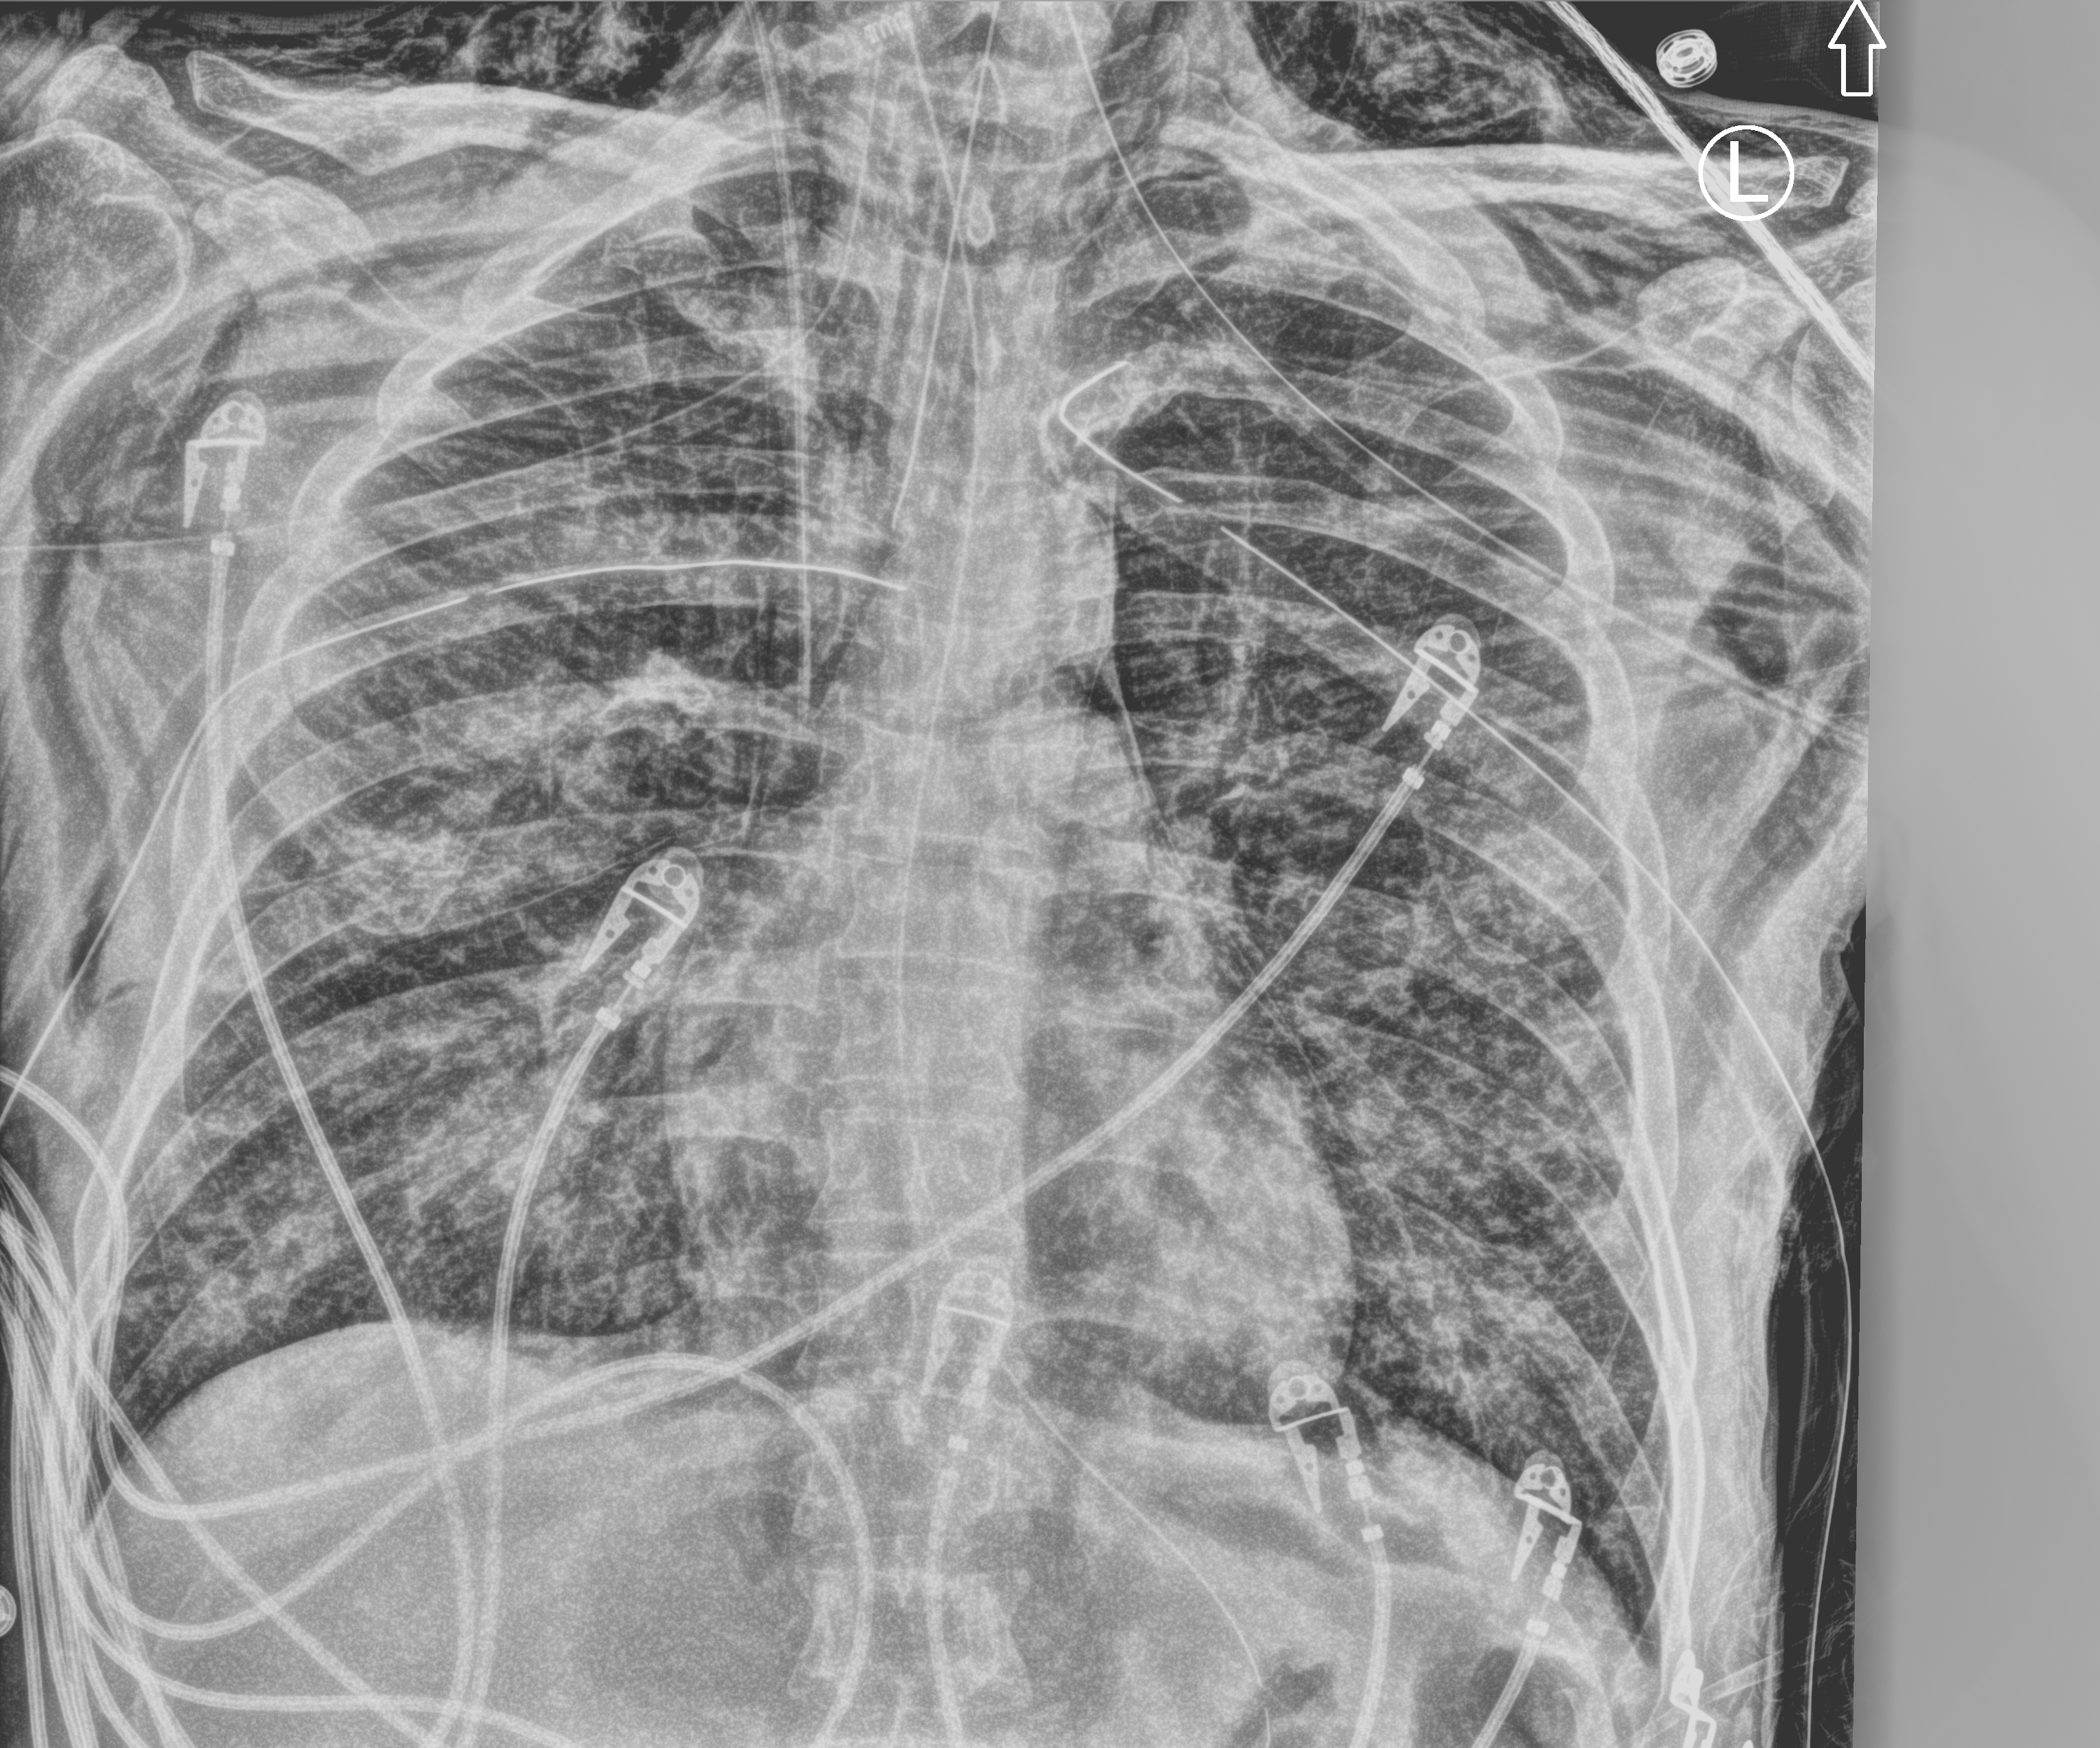
Chest X-ray (portable); anteroposterior (AP) projection. Patient hospitalised with COVID-19; male, aged 18–59 years.
From the hospital-stay record, not from the radiograph (when in the stay this image was taken is not recorded):
- chronic kidney disease (admission record): no
- other chronic lung disease (admission record): no
- mechanically ventilated during this hospital stay: yes